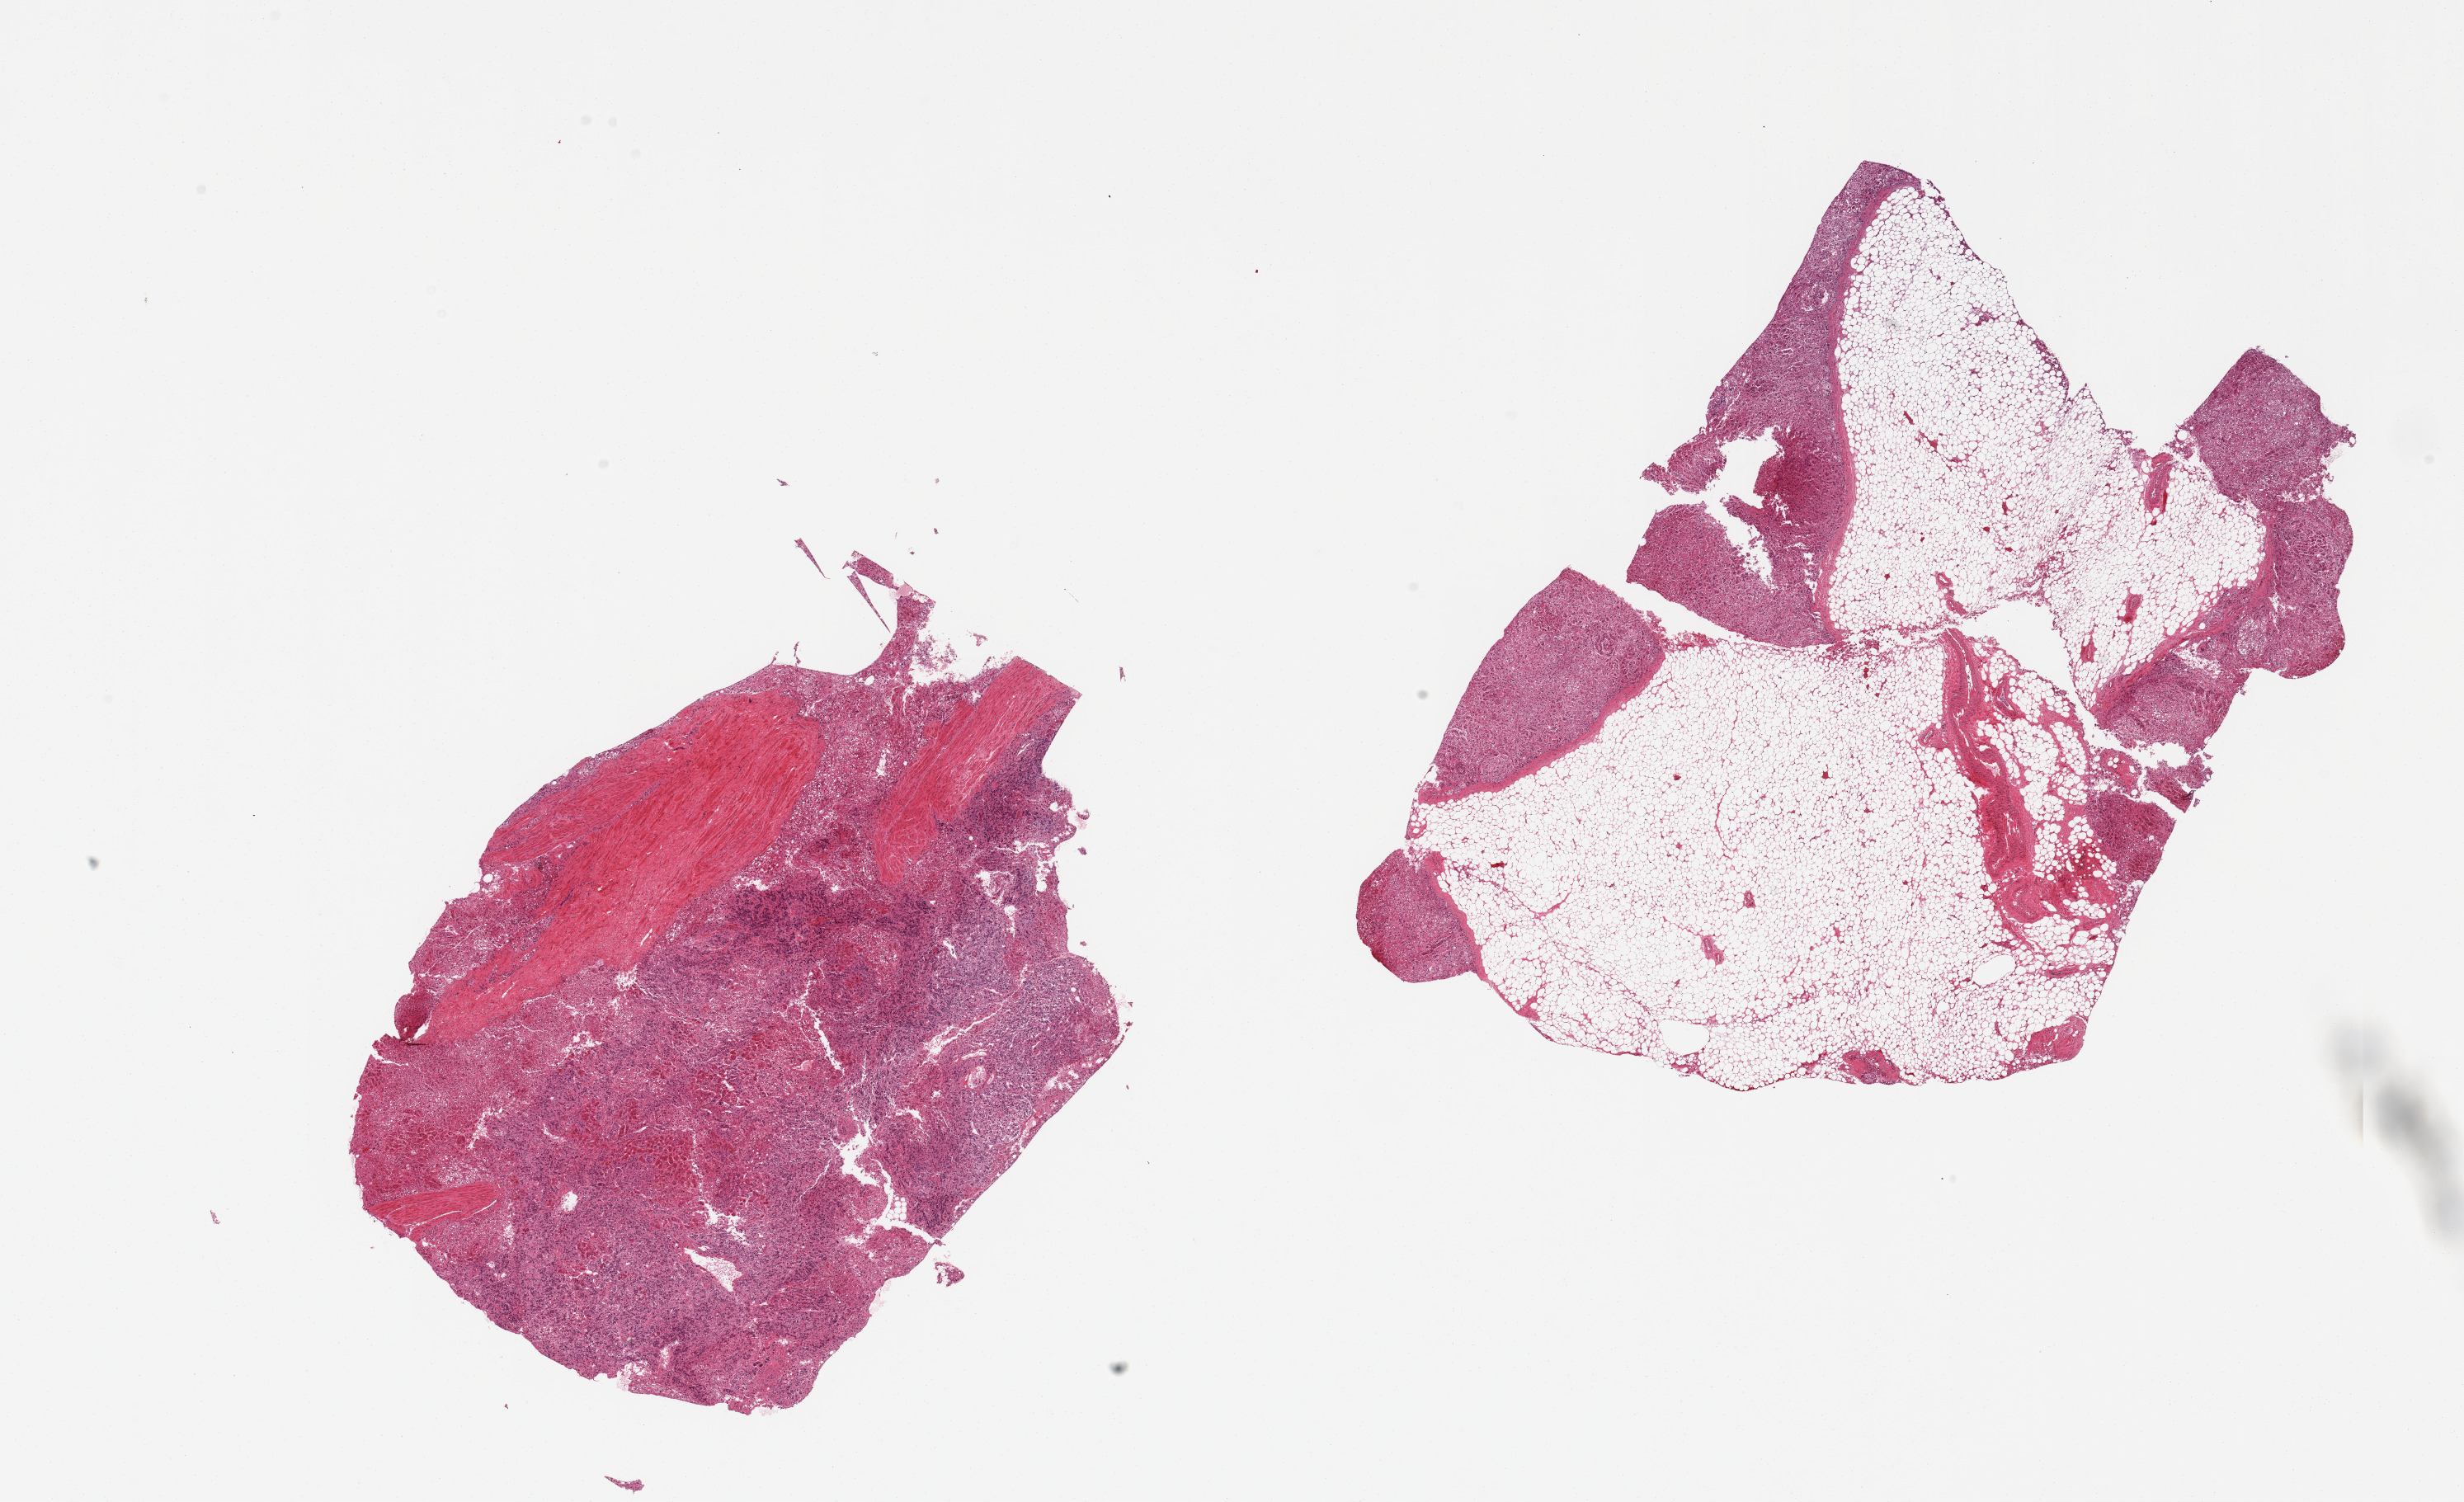
Whole-slide image, H&E stain, shown as a low-resolution overview of the whole scanned area (about 23.6 x 14.4 mm, slide scanned at 20x); PAXgene-fixed paraffin-embedded (PFPE) section; sampled site (target tissue): adrenal gland; donor tissue sample. Donor: male.
- reviewer comment on this tissue sample: 2 pieces: 1 with 80% fat, other with 20% vascular muscle